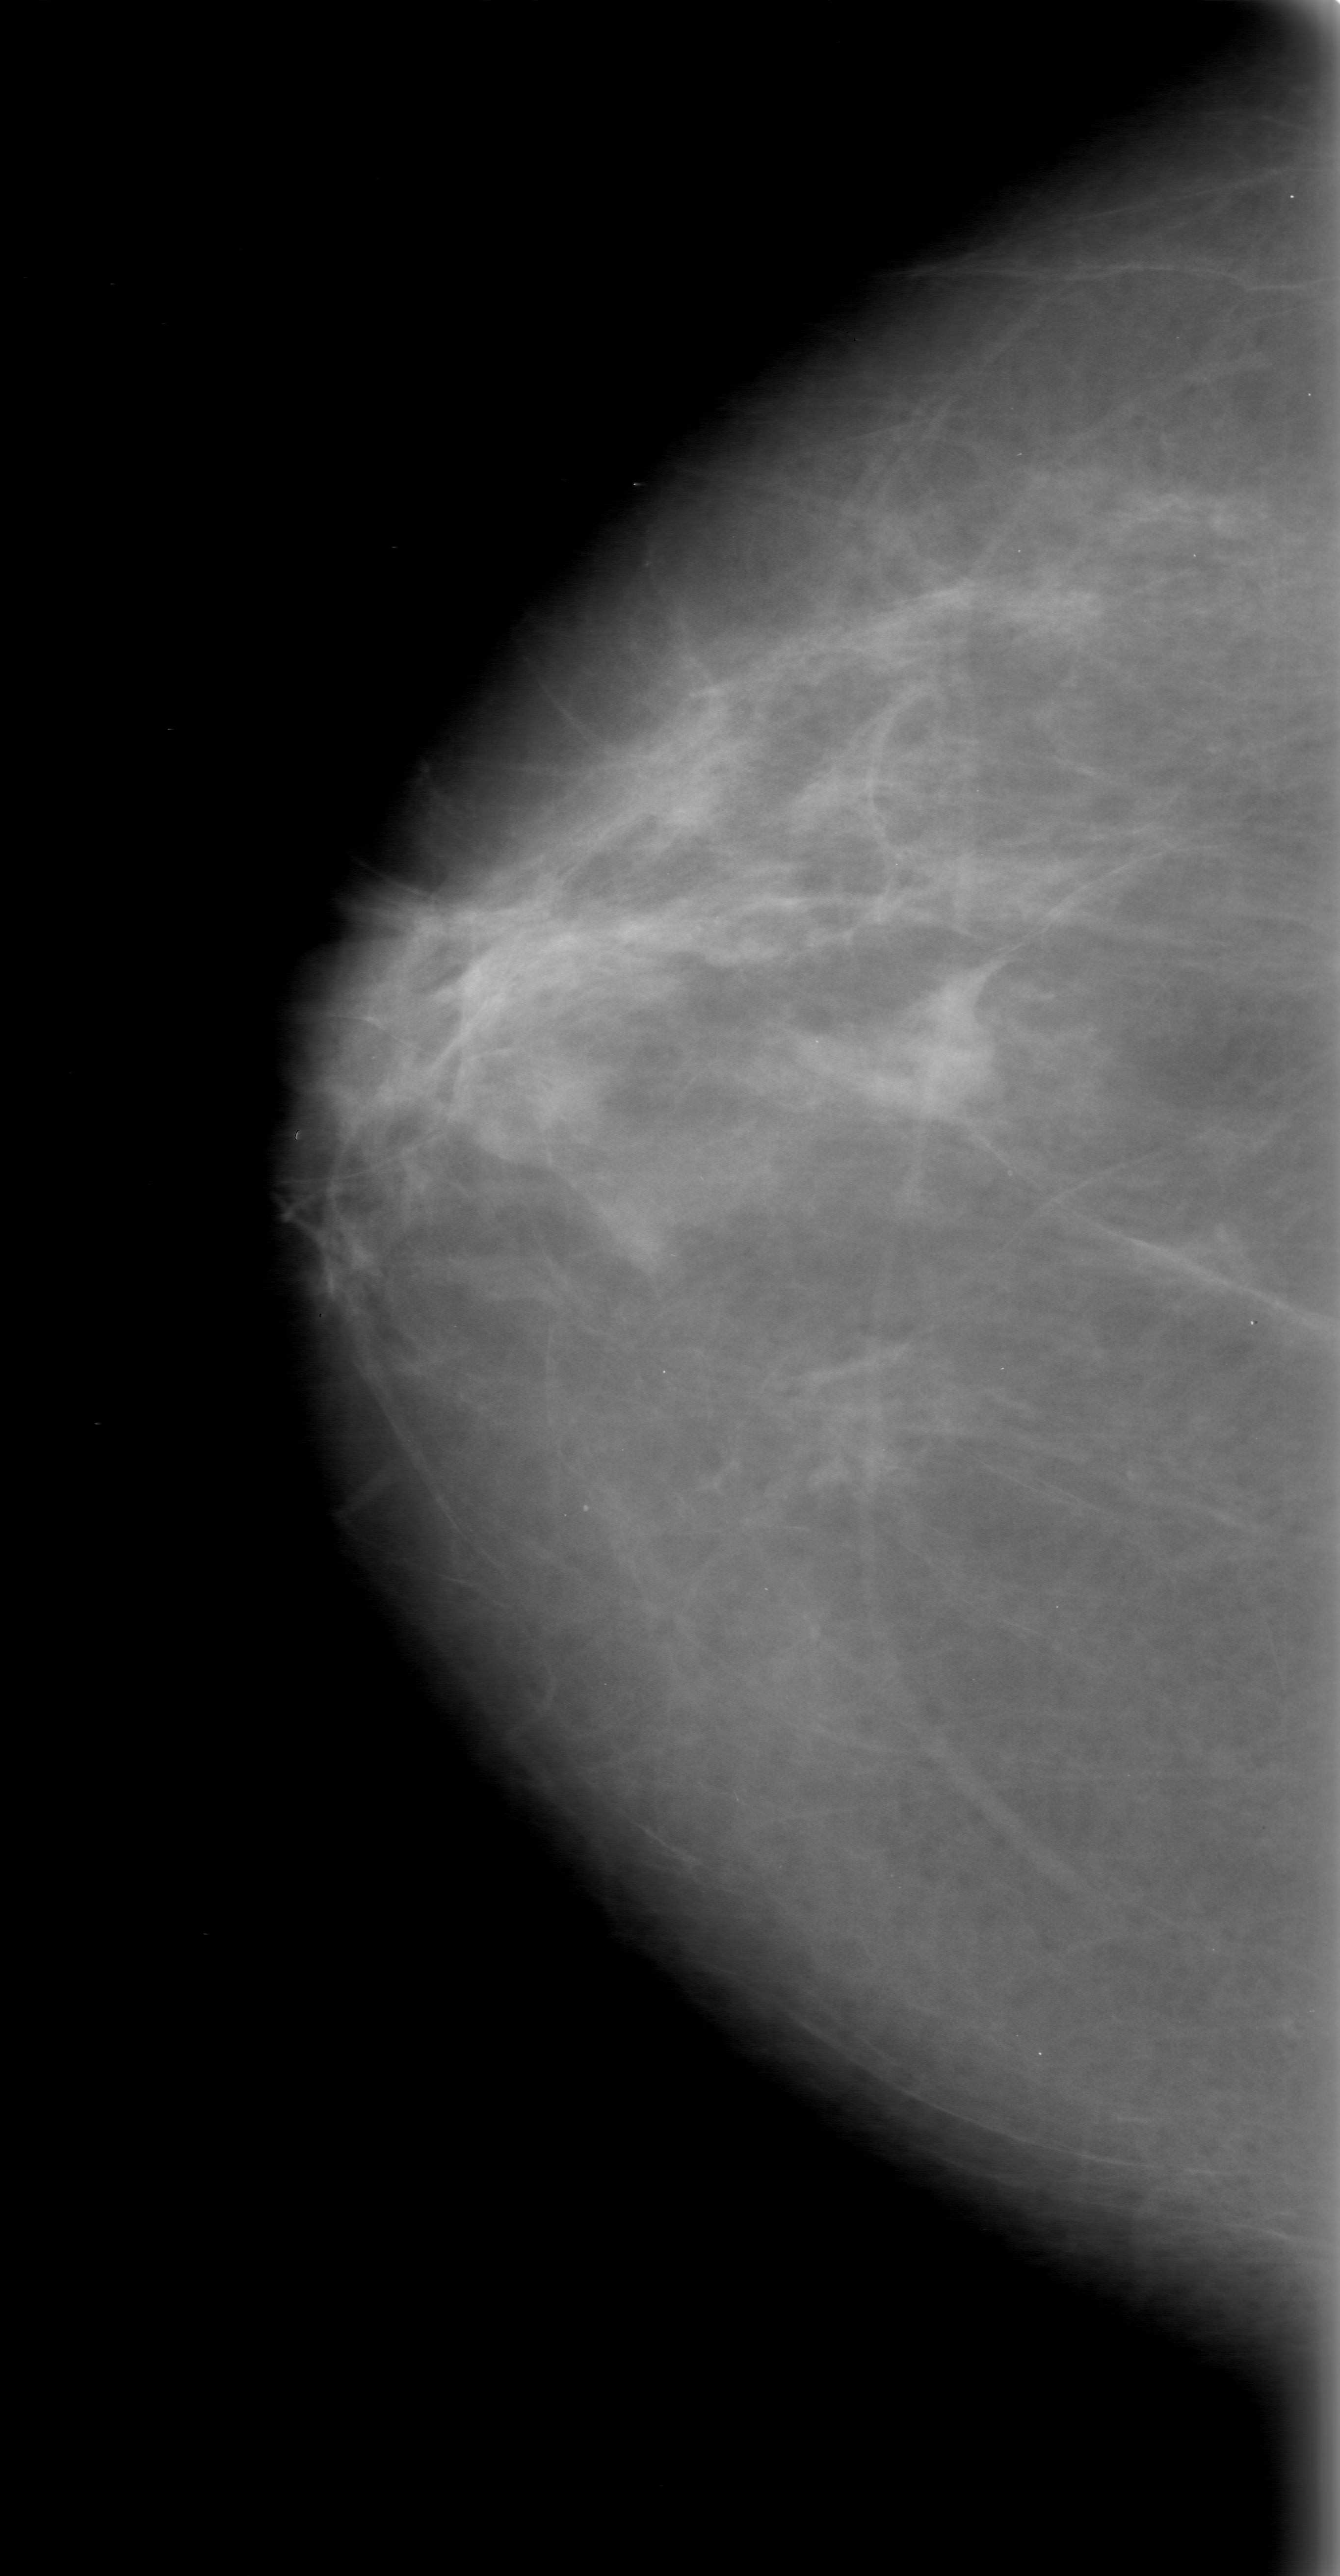
Digitized screen-film mammogram; right breast; CC view; BI-RADS breast density category 2 (scale 1–4).
- Finding: mass, shape irregular, margins obscured; BI-RADS assessment category 0 (incomplete: needs additional imaging); subtlety rating 5 on a 1 (subtle) to 5 (obvious) scale; pathology result (as recorded, not read from the image): benign.